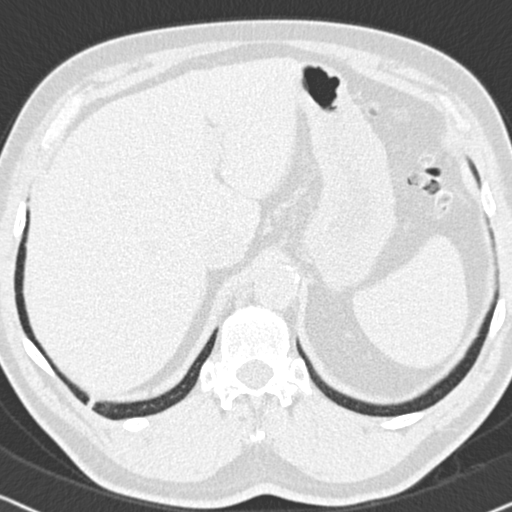
Axial slice from a low-dose chest CT screening exam, baseline screening round, lung window (W 1500 / L -600 HU), standard (soft-tissue) reconstruction kernel (B30f), 120 kVp, 512 × 512 image matrix. Male participant, aged 63 years at enrolment.
• Lesion marked by an expert reader, bounding box <73,391,104,417> (left, top, right, bottom; pixels).
• No non-calcified nodule or mass ≥4 mm was recorded by the screening reader at this exam.
• Later outcome: lung cancer diagnosed 626 days after this screen (after the second annual screen) — adenocarcinoma, NOS, right lower lobe, moderately differentiated (G2), stage IIIB (AJCC 6th edition), 17 mm at pathology.